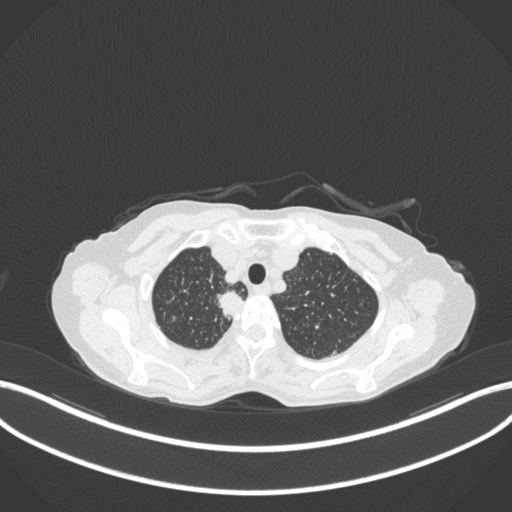
Chest CT, one axial slice. Position 319 of 363 along the scan axis. Reconstruction kernel B31f. 120 kVp. Lung window (W 1500 / L -600 HU). 1 mm slice thickness. 512 × 512 image matrix, field of view 400 × 400 mm. Patient: female, 75 years. From the clinical record (not read from this slice): clinical TNM (as recorded): T1c N1 M1.
Outlined on this slice (bounding box drawn by a radiologist):
- lung tumour (recorded histology: adenocarcinoma): bounding box [x1, y1, x2, y2] px = [214, 288, 246, 322]